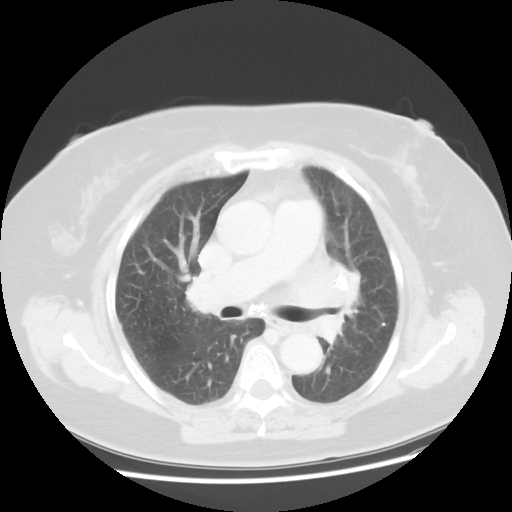
Chest CT, one axial slice; slice 27 of 49 in the series (ordered by position); reconstruction kernel STANDARD; 120 kVp; lung window (W 1500 / L -600 HU); 5 mm slice thickness; 512 × 512 image matrix, field of view 374 × 374 mm. Patient: female, 58 years. From the clinical record (not read from this slice): clinical TNM (as recorded): T4 N3 M0; histopathological grade: G3.
Structures marked on this image (bounding box drawn by a radiologist):
- lung tumour (recorded histology: small cell carcinoma): bounding box [x1, y1, x2, y2] px = [295, 256, 375, 336]